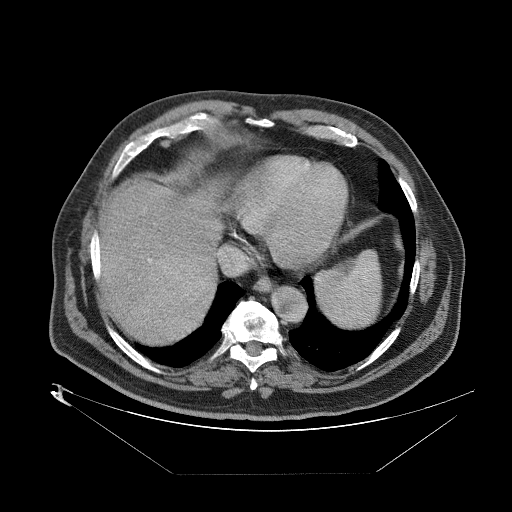
Contrast-enhanced abdominal CT (liver protocol), one axial slice; position 73 of 89 along the scan axis; reconstruction kernel STANDARD; 140 kVp; one of 2 acquisitions stored at this slice position; soft-tissue window (W 400 / L 40 HU); 2.5 mm slice thickness; 512 × 512 image matrix. From the clinical record (not read from this slice): diagnosis: hepatocellular carcinoma (patient treated with transarterial chemoembolisation; whether this scan precedes or follows treatment is not stated here); TNM stage (as recorded): Stage-II; Child-Pugh class: B; tumour nodularity: multinodular.
Outlined on this slice (semi-automatically segmented with operator editing):
- abdominal aorta: bounding box (x1, y1, x2, y2) in pixels: (270, 287, 305, 321)
- liver parenchyma outside the tumour (the mass and vessels are separate outlines, so this box may not span the whole liver): (94, 174, 220, 340)
- mass: (145, 253, 214, 329)
- liver vessels: (95, 260, 148, 275)